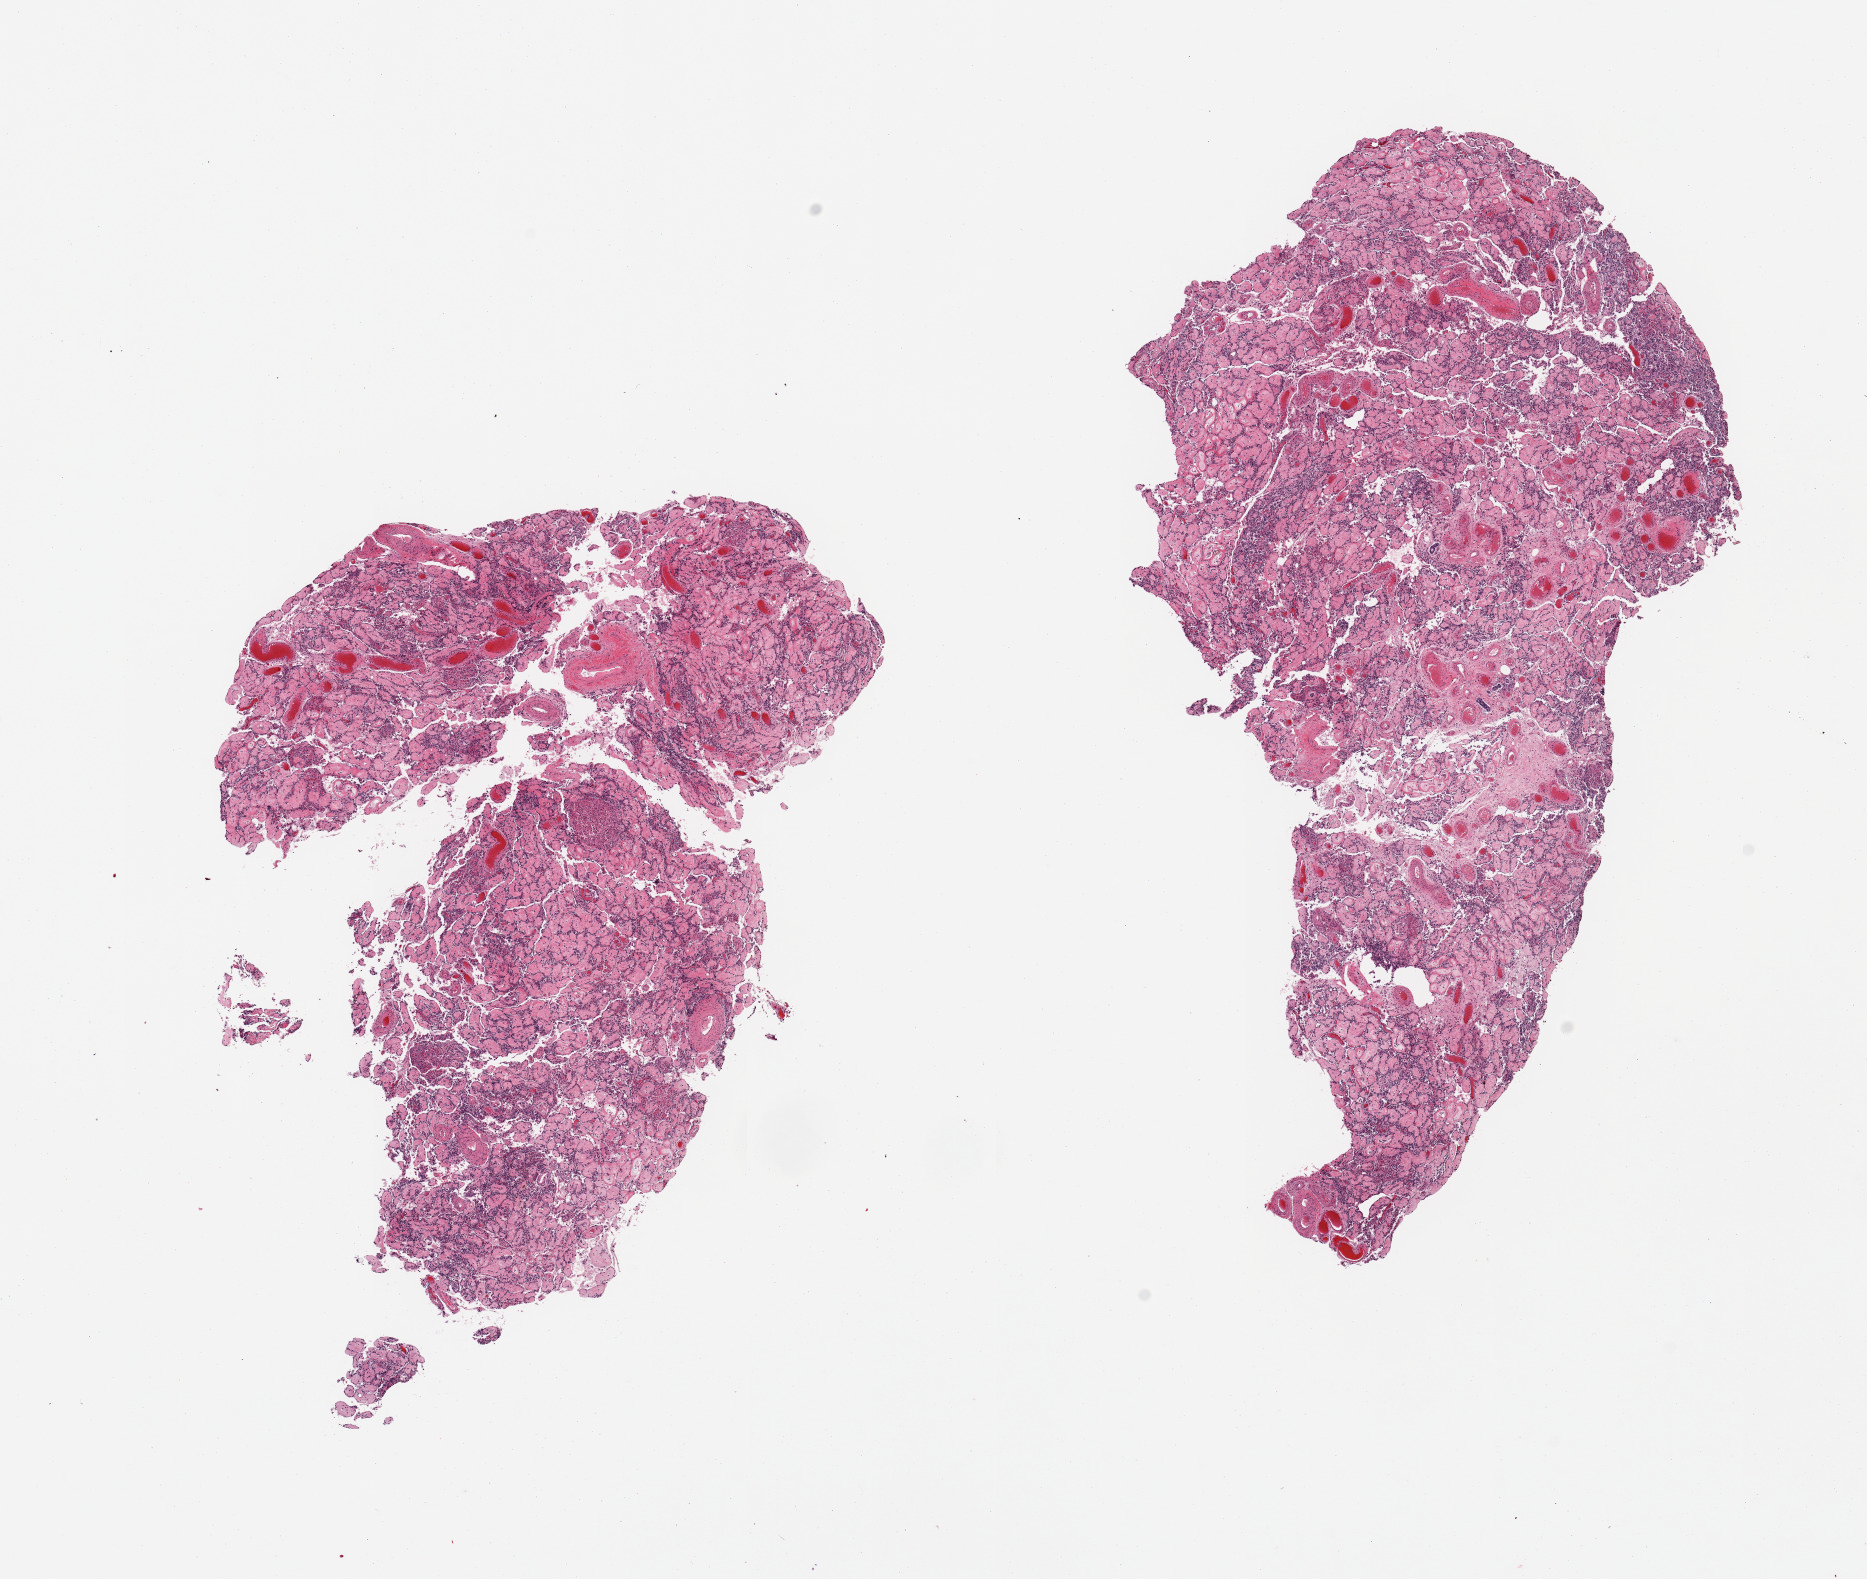
Digitized H&E-stained section, whole scanned area (about 14.8 x 12.5 mm, acquisition: 20x scan) shown as a low-resolution overview, PAXgene-fixed paraffin-embedded (PFPE) section, section of testis (target tissue), tissue donor sample. Donor sex: male.
Review note (as recorded): 2 pieces; complete tubular sclerosis, absent spermatogenesis; Leydig cell hyperplasia; possible Klinefelter syndrome.